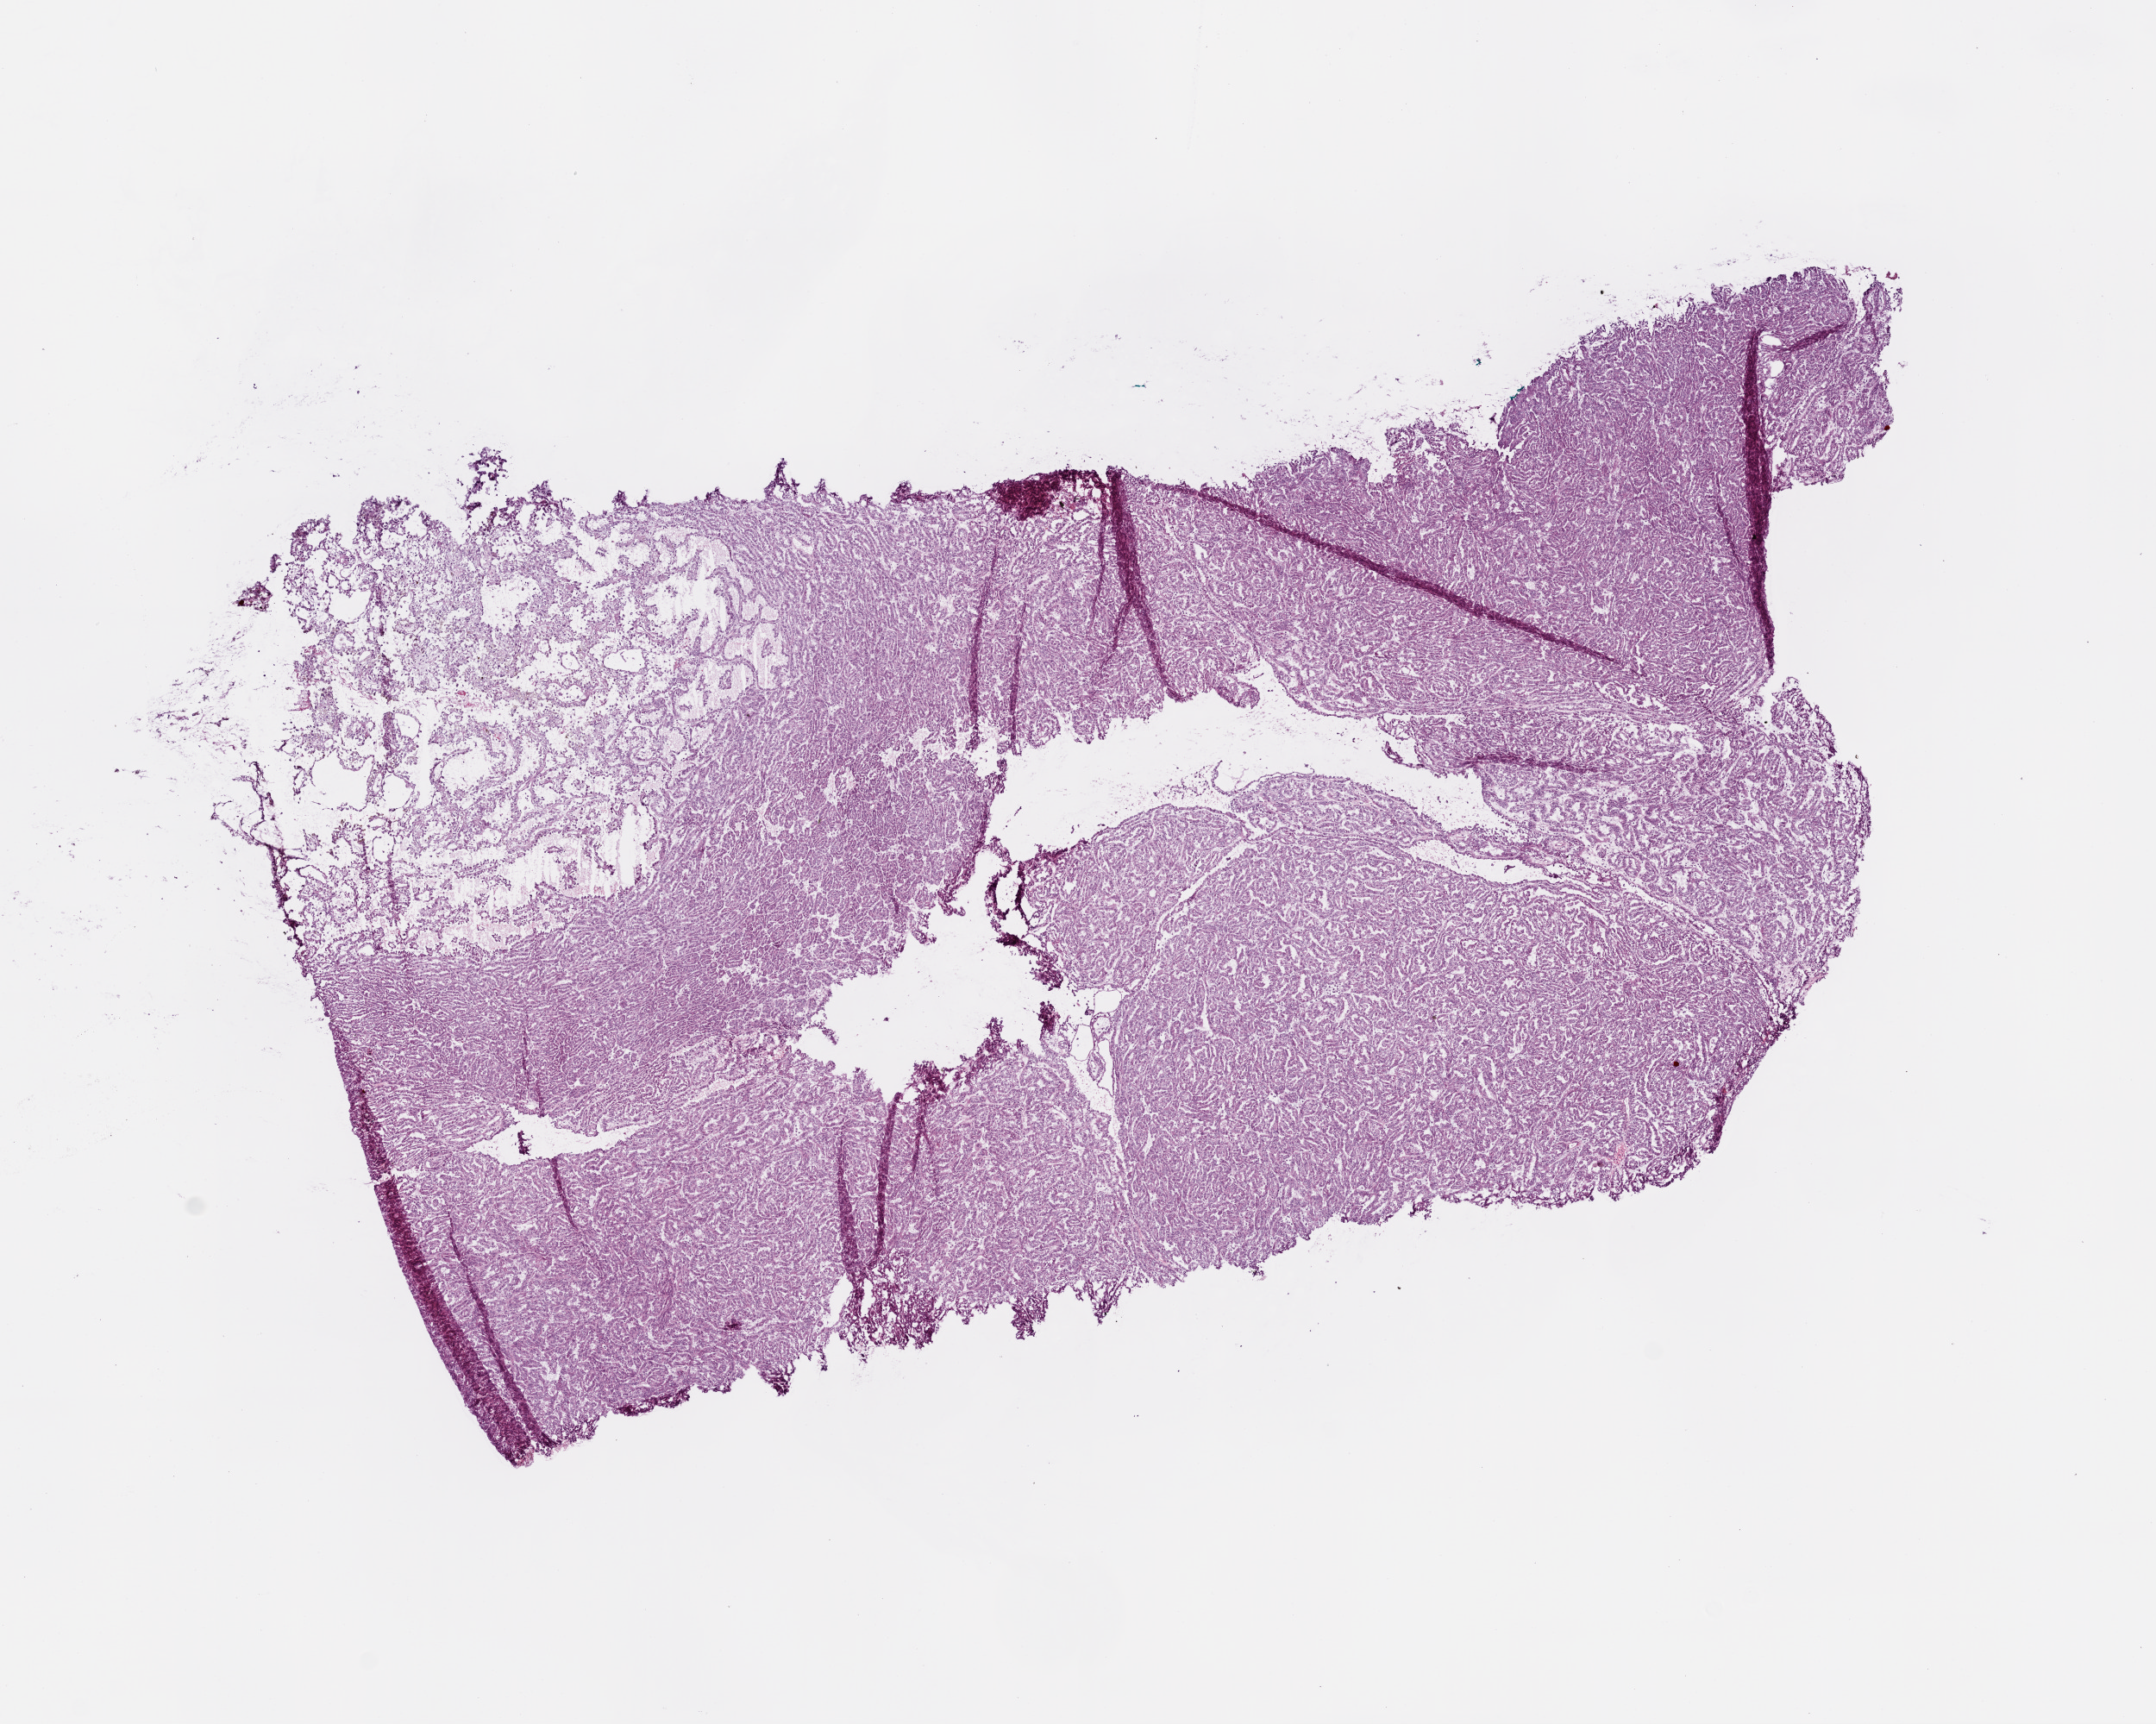
Whole-slide histology image, H&E, shown as a low-resolution overview of the whole scanned area (about 10.0 x 8.0 mm, from a 20x scan), frozen section from the top of the tissue portion, sample: primary tumour, kidney. Male patient; age at initial diagnosis 71 years. Composition of this section per pathologist review: tumour cells 95%, tumour nuclei 90%, normal cells 0%, stromal cells 5%, necrosis 0%.
• TNM: T3a NX
• histologic diagnosis: Papillary adenocarcinoma, NOS
• AJCC pathologic stage: III